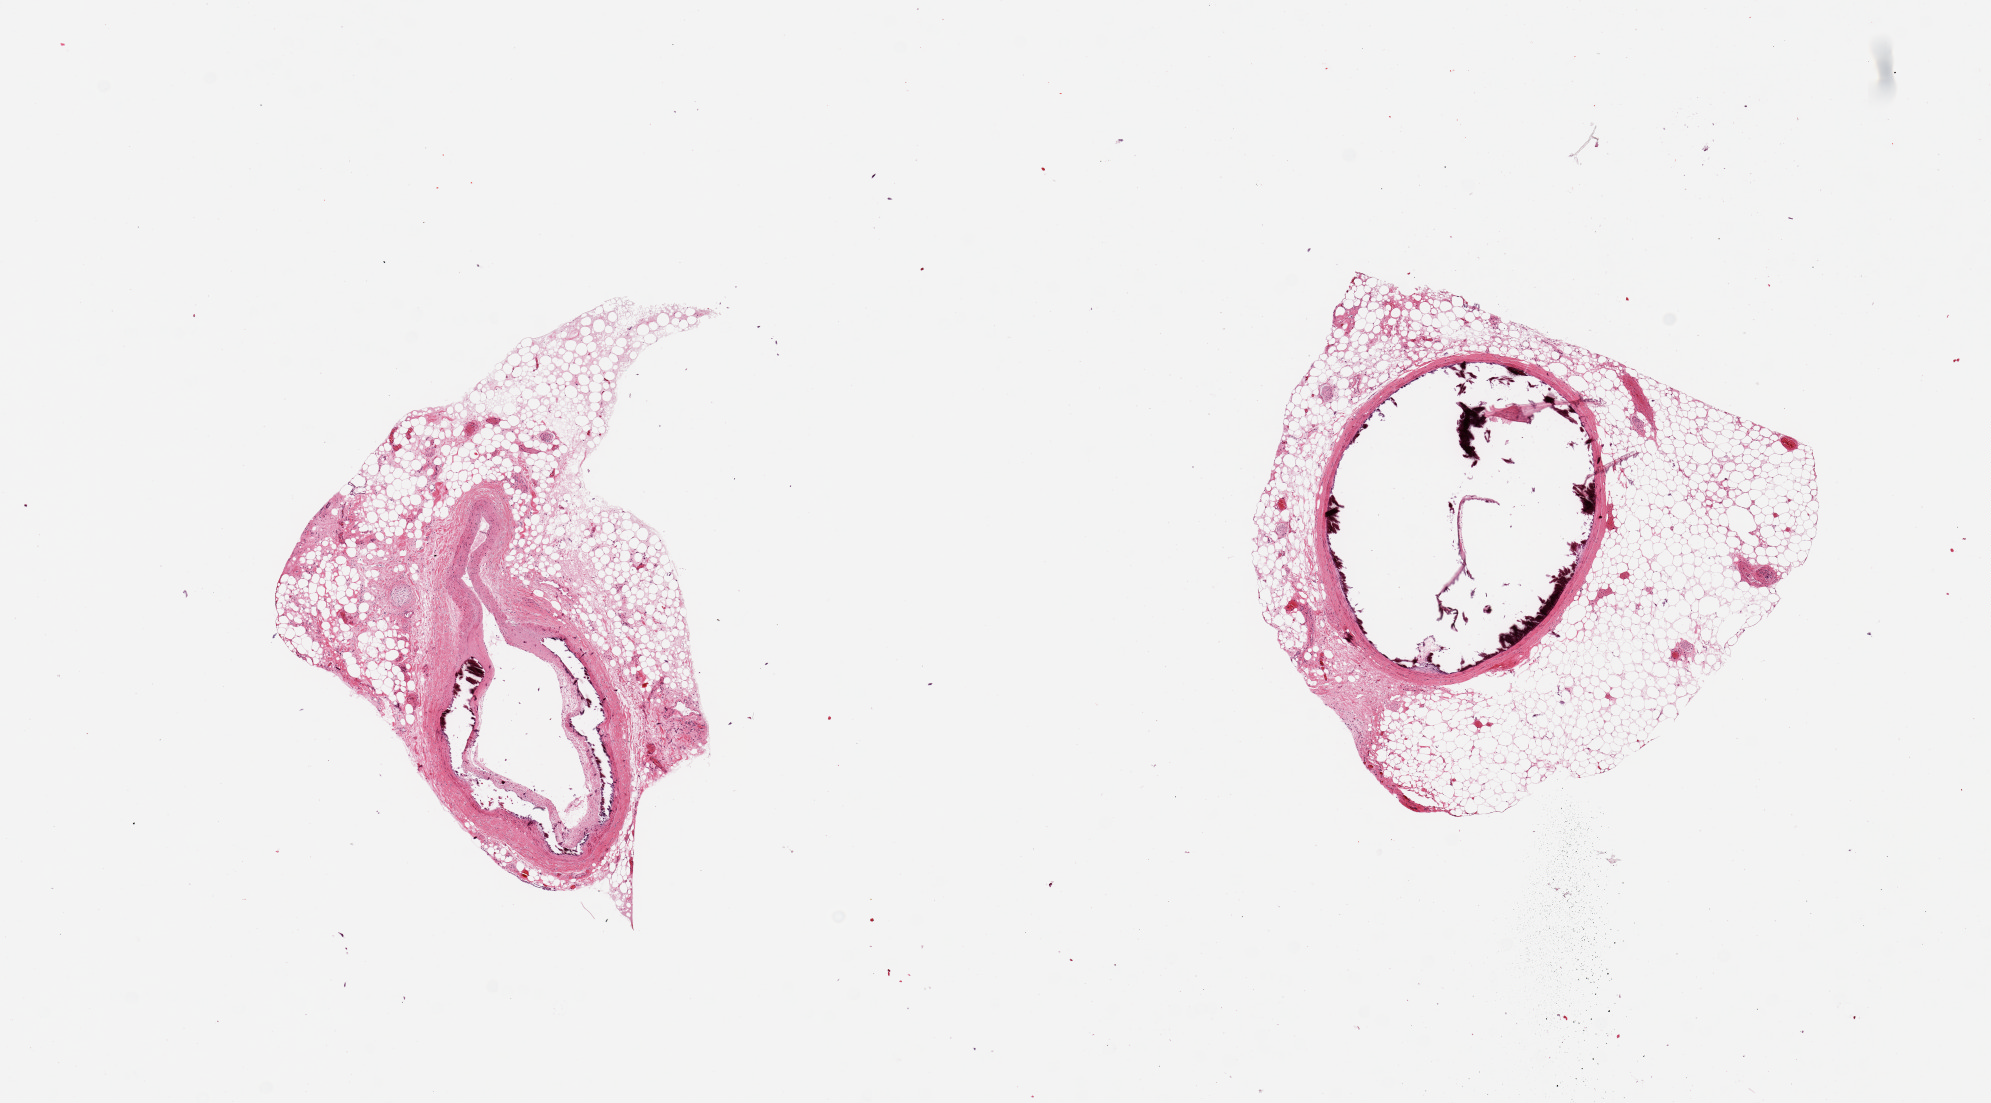
Whole-slide image, haematoxylin and eosin stain, shown as a low-resolution overview of the whole scanned area (about 15.8 x 8.7 mm, from a 20x scan); PAXgene-fixed paraffin-embedded (PFPE) section; sampled site (target tissue): coronary artery; tissue donor sample. Donor: female.
Pathologist's review note for this sample: 2 pieces, peripheral rim of fat measuring up to 1.4mm in thickness, calcific atherosclerosis, one piece not intact with rim of vessel with fragments of calcified material.